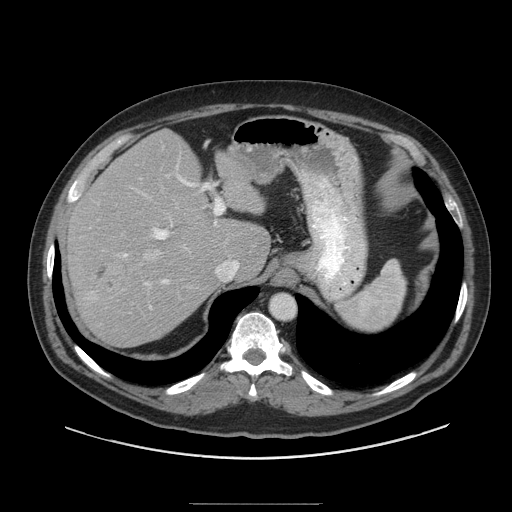
Contrast-enhanced abdominal CT (liver protocol), one axial slice. Position 69 of 91 along the scan axis. 140 kVp. Soft-tissue window (W 400 / L 40 HU). 512 × 512 image matrix, field of view 440 × 440 mm. Case-level facts recorded for this patient, not image findings: diagnosis: hepatocellular carcinoma (patient treated with transarterial chemoembolisation; whether this scan precedes or follows treatment is not stated here); TNM stage (as recorded): Stage-I; Child-Pugh class: A; tumour differentiation: well differentiated; tumour nodularity: uninodular.
Structures marked on this image (semi-automatically segmented with operator editing):
- abdominal aorta: bounding box (x1, y1, x2, y2) in pixels: (272, 295, 295, 319)
- liver parenchyma outside the tumour (the mass and vessels are separate outlines, so this box may not span the whole liver): (66, 130, 268, 346)
- mass: (90, 256, 128, 296)
- liver vessels: (123, 175, 239, 309)